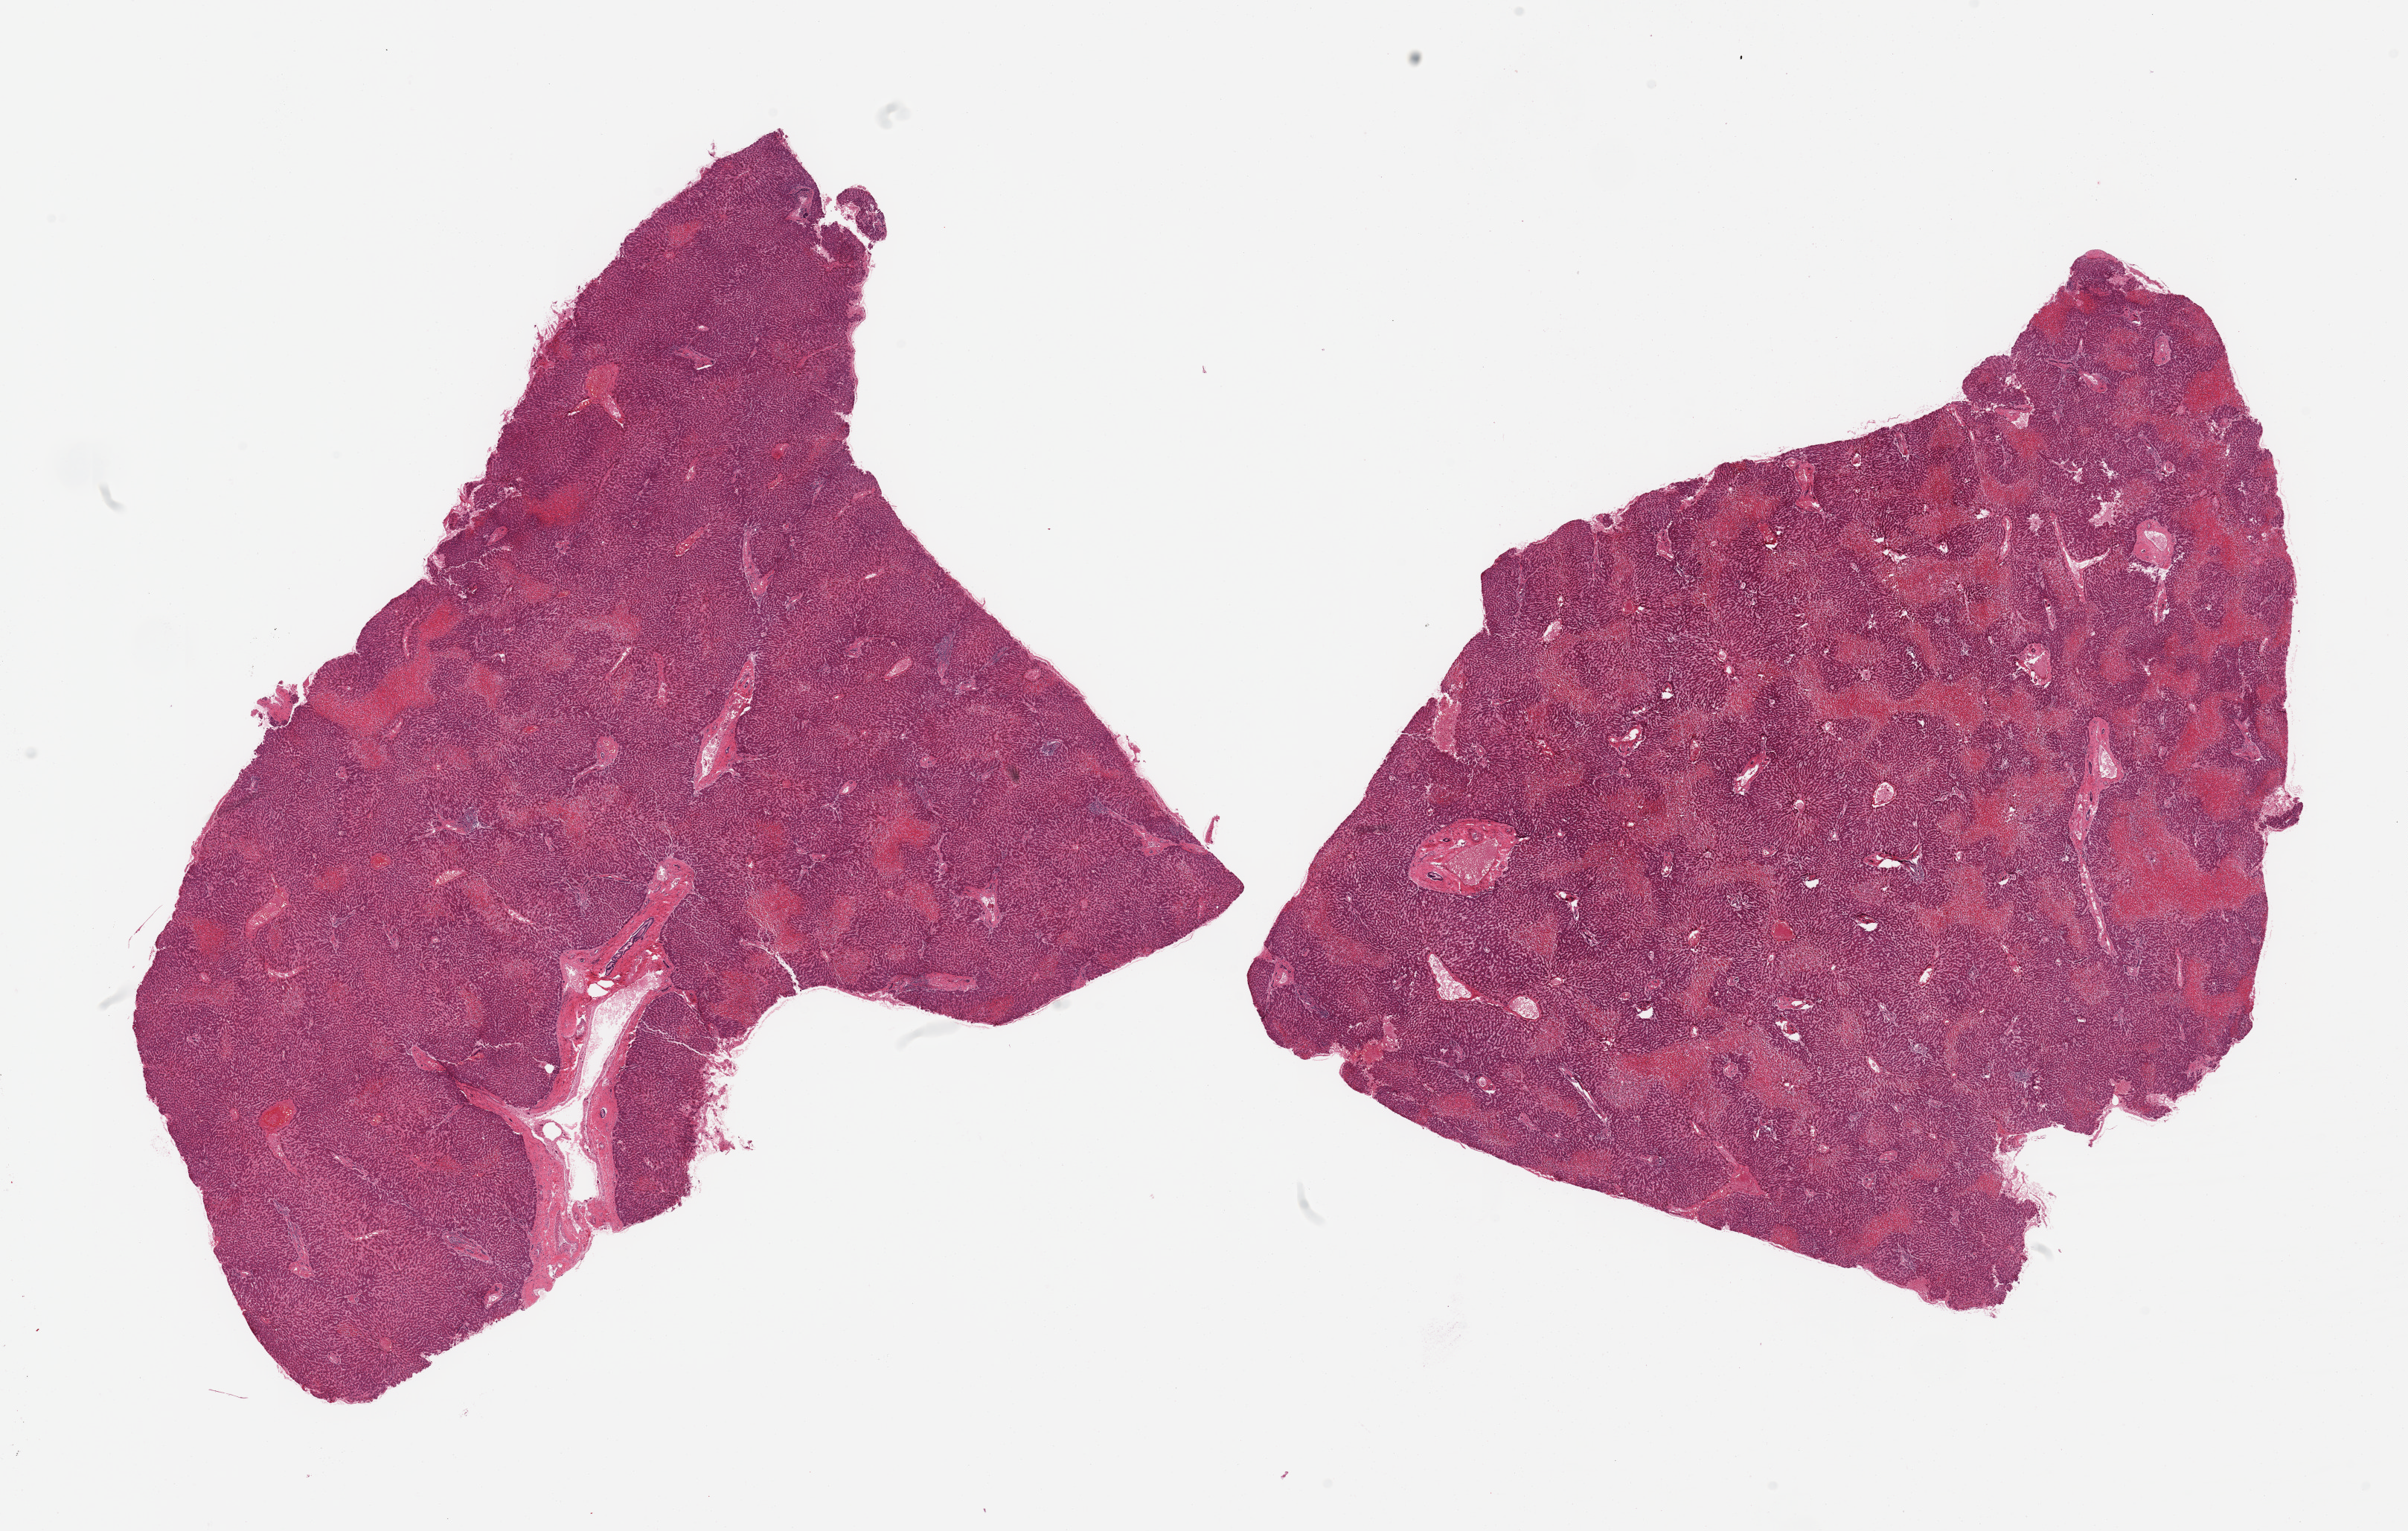
Digitized H&E-stained section — a low-resolution overview of the entire scanned area, about 25.6 x 16.3 mm, PAXgene-fixed paraffin-embedded (PFPE) section, sampled site (target tissue): liver, donor tissue sample. Donor sex: male.
Reviewer comment on this tissue sample: 2 pieces, moderate cardiac congestion.